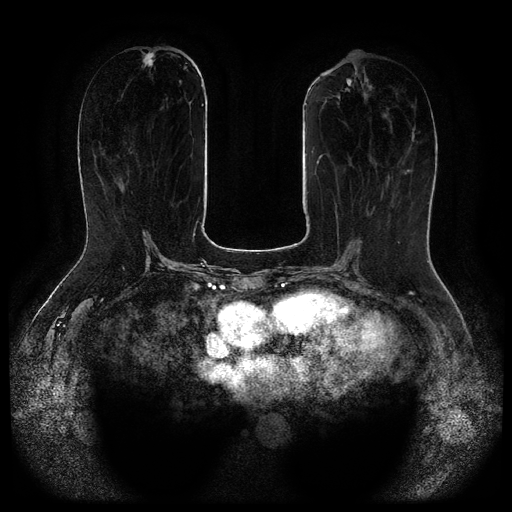
Breast MRI (dynamic contrast-enhanced, multi-phase), one axial slice; dynamic contrast-enhanced series, time point 2 of 5 at this slice position (early post-contrast); 1.5 T; TE 2.6 ms, TR 5.3 ms; 2.1 mm slice thickness; 512 × 512 image matrix. Female patient, age 65 years.
Outlined on this slice (semi-automatic segmentation, software-assisted and operator-edited):
- breast lesion (labelled 'tumour' in the annotation; benign lesions carry a separate 'benign' label): box from (x=143, y=52) to (x=154, y=66) px